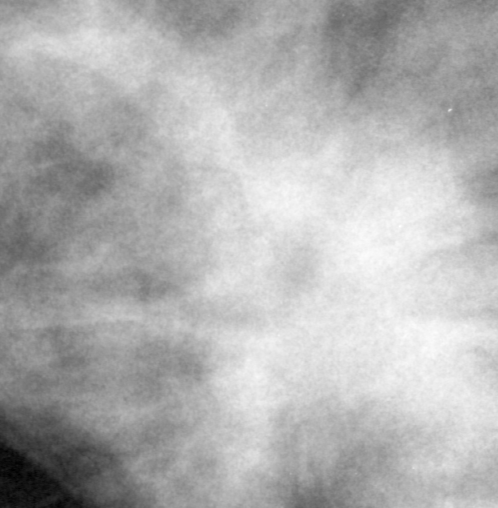
Crop from a digitized film mammogram around one marked abnormality, right breast, CC view.
Finding: mass, shape irregular, margins spiculated; BI-RADS assessment category 5; pathology (as recorded): malignant.